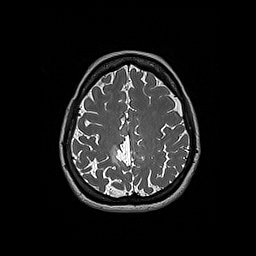
Brain MRI from a brain-tumour surgery series, one axial slice; position 59 of 192 along the scan axis; 256 × 256 image matrix. From the clinical record (not read from this slice): histopathology: Oligodendroglioma; WHO grade: 2; IDH mutation: yes.
Structures marked on this image (expert manual segmentation):
- tumour: box from (x=110, y=145) to (x=119, y=166) px